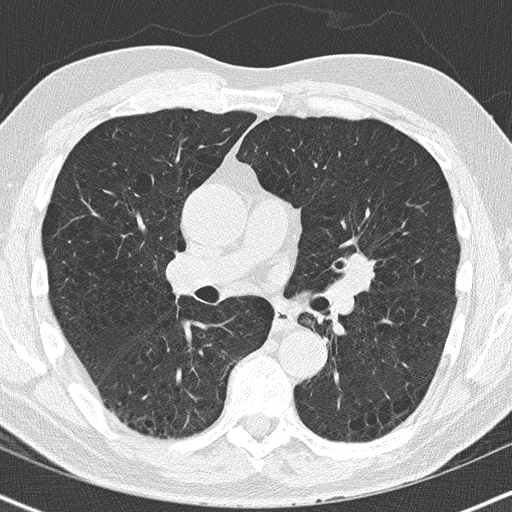
Low-dose screening chest CT, one axial slice; position 87 of 163 along the scan axis; reconstruction kernel B50f; 120 kVp; lung window (W 1500 / L -600 HU); 2 mm slice thickness; 512 × 512 image matrix.
Structures marked on this image (expert manual segmentation):
- lesion 1 (tumor, upper lobe of left lung): bounding box <343,251,376,295> (left, top, right, bottom; pixels)